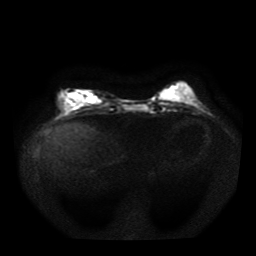
Breast MRI, one axial slice. Position 13 of 41 along the scan axis. Diffusion-weighted series; image 2 of 4 stored at this slice position (different b-values; order by instance number). 1.5 T. 5 mm slice thickness. 256 × 256 image matrix. Female patient.
Structures marked on this image (manually delineated by an expert):
- tumour on diffusion-weighted imaging: bounding box [x1, y1, x2, y2] px = [66, 92, 95, 104]